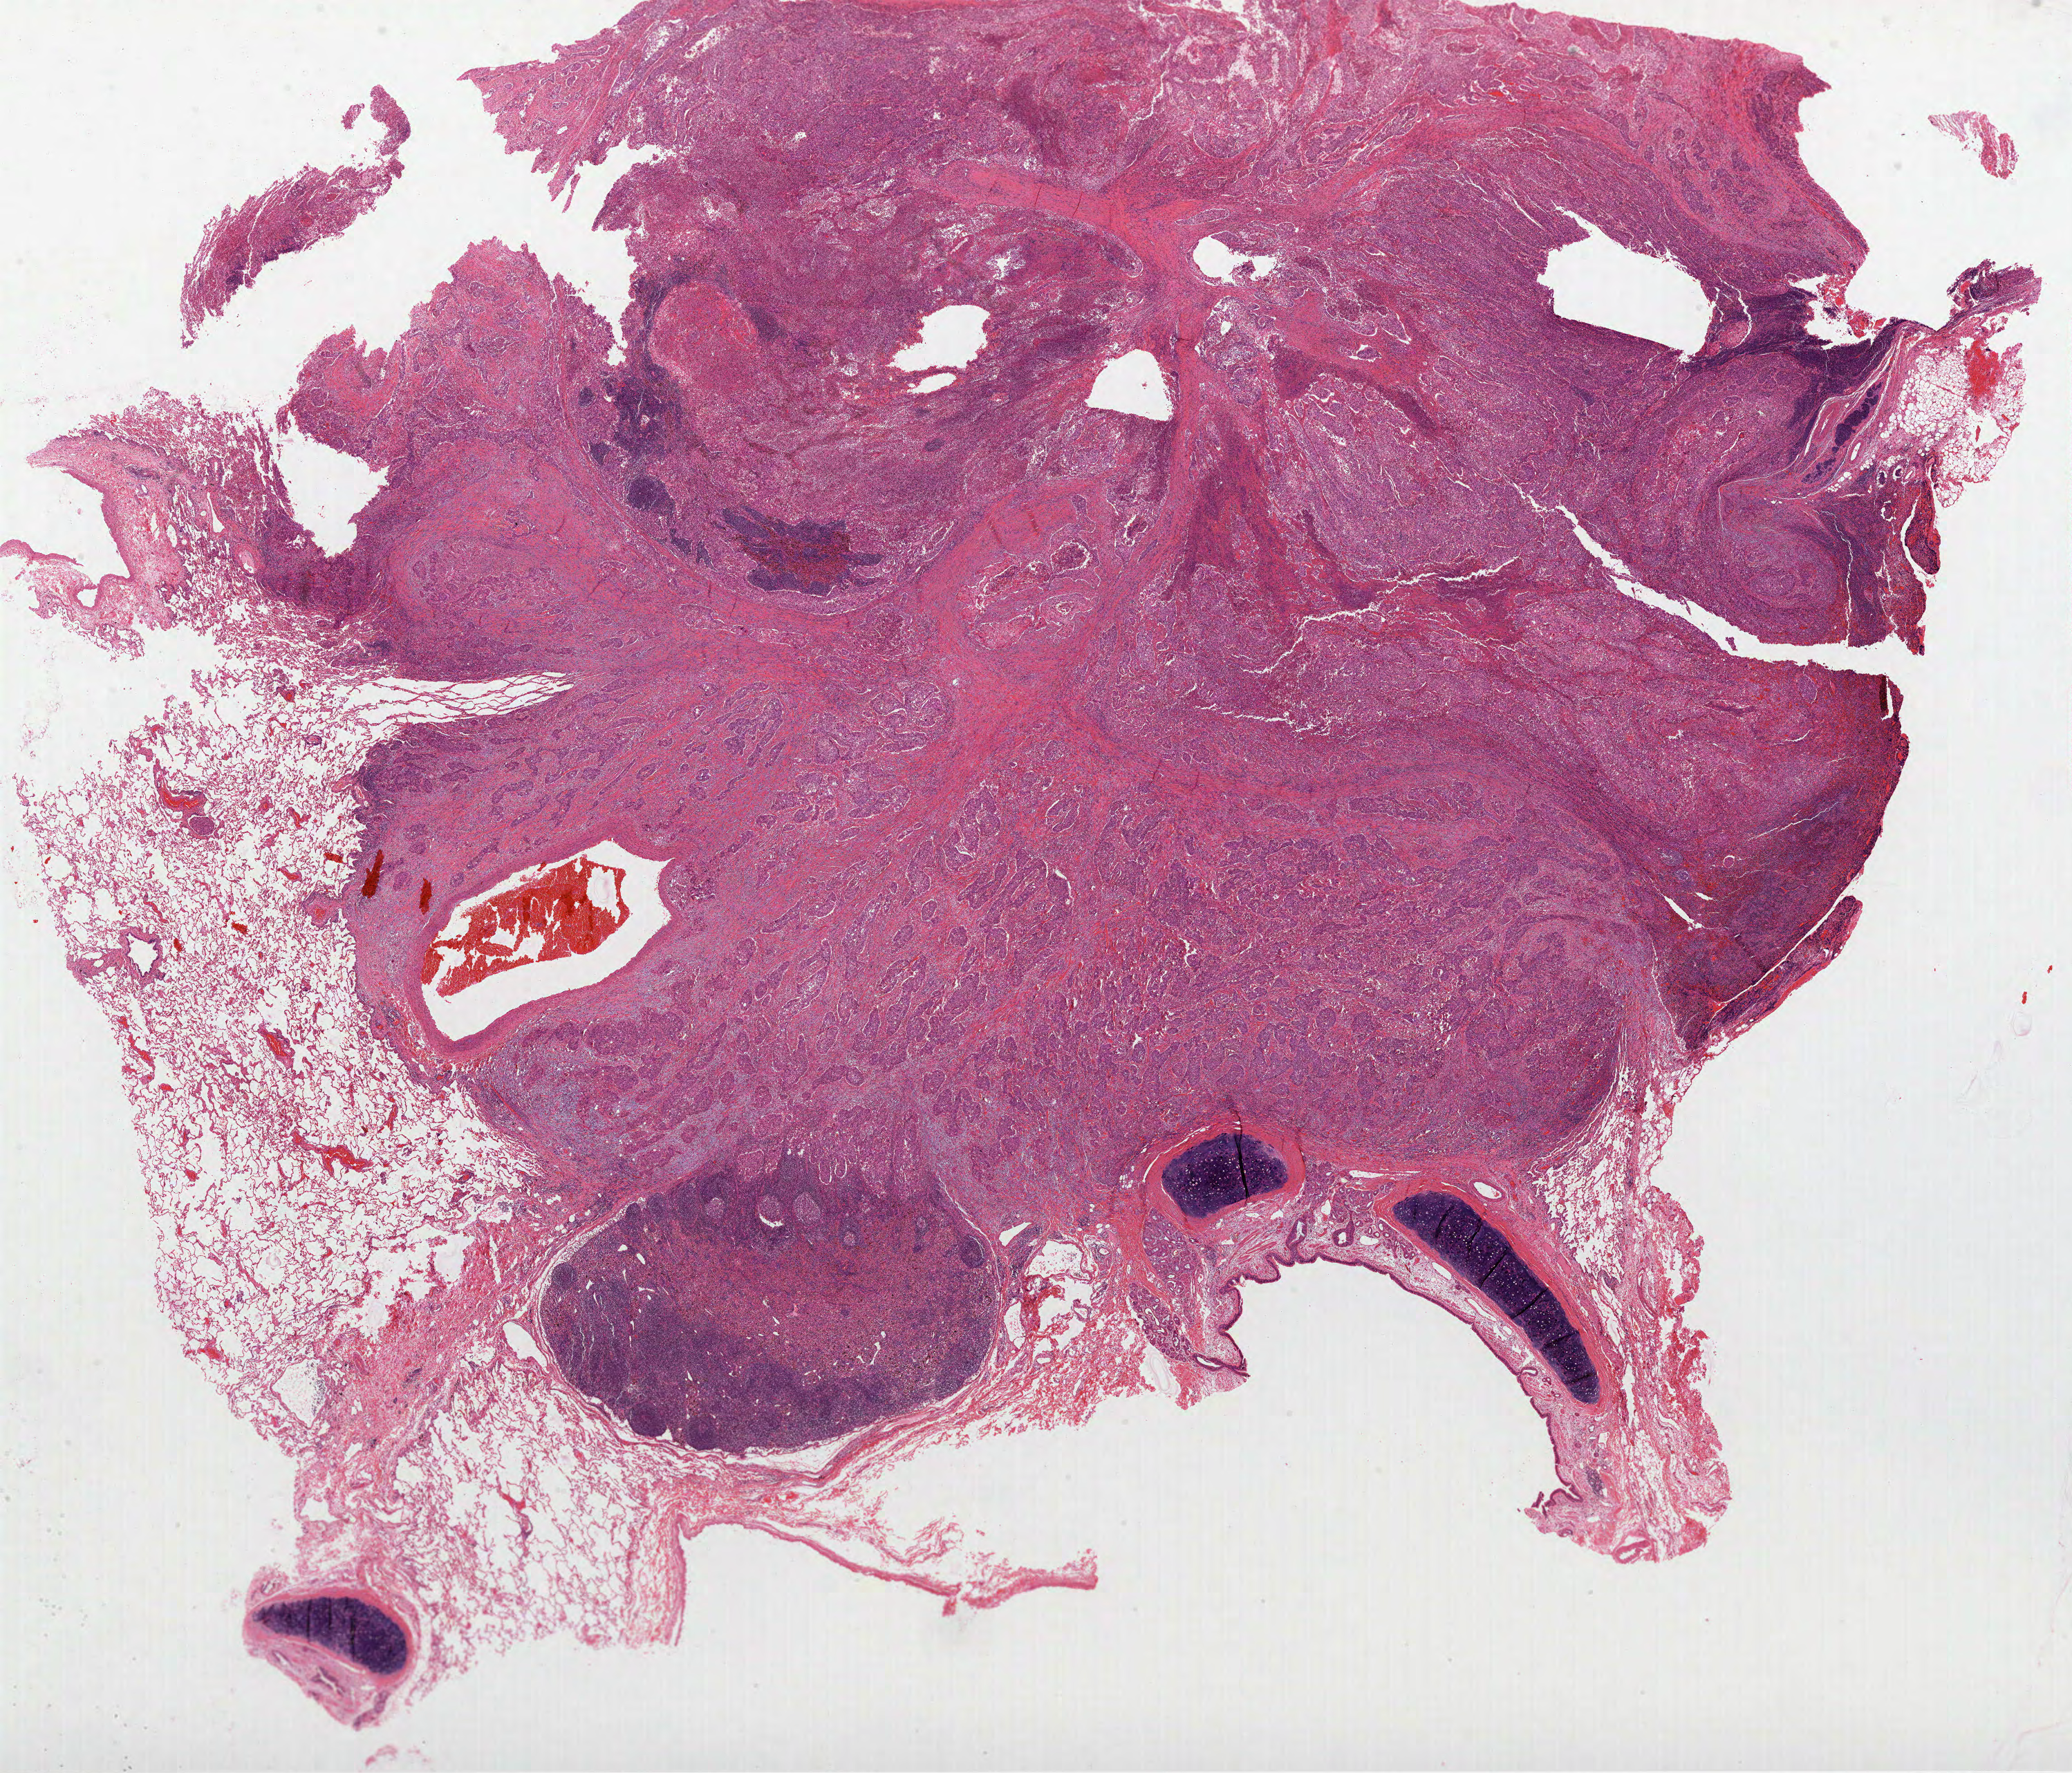
H&E-stained whole-slide image — whole scanned area (about 24.2 x 20.7 mm, acquisition: 40x scan) shown as a low-resolution overview. Formalin-fixed paraffin-embedded (FFPE) diagnostic section. Lung, primary tumour sample. Female patient; age at initial diagnosis 45 years.
AJCC pathologic stage: IIA (7th edition). Laterality: right. Pathologic diagnosis: Squamous cell carcinoma, NOS (upper lobe, lung).